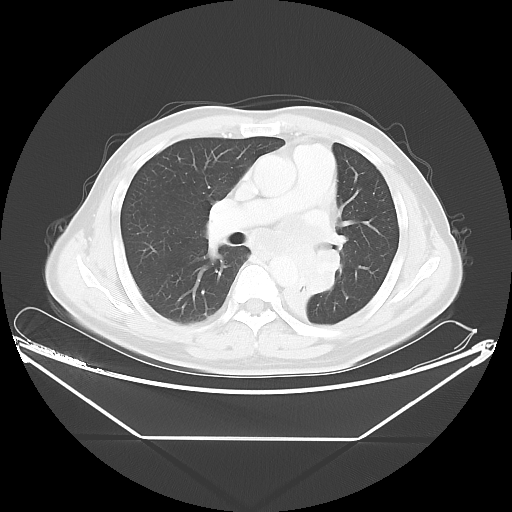
Chest CT, one axial slice. Slice 26 of 48 in the series (ordered by position). Reconstruction kernel LUNG. 120 kVp. Lung window (W 1500 / L -600 HU). 512 × 512 image matrix. Male patient, age 58 years. Case-level facts recorded for this patient, not image findings: clinical TNM (as recorded): T3 N3 M0.
Outlined on this slice (bounding box drawn by a radiologist):
- lung tumour (recorded histology: squamous cell carcinoma): bounding box [x1, y1, x2, y2] px = [278, 230, 355, 343]